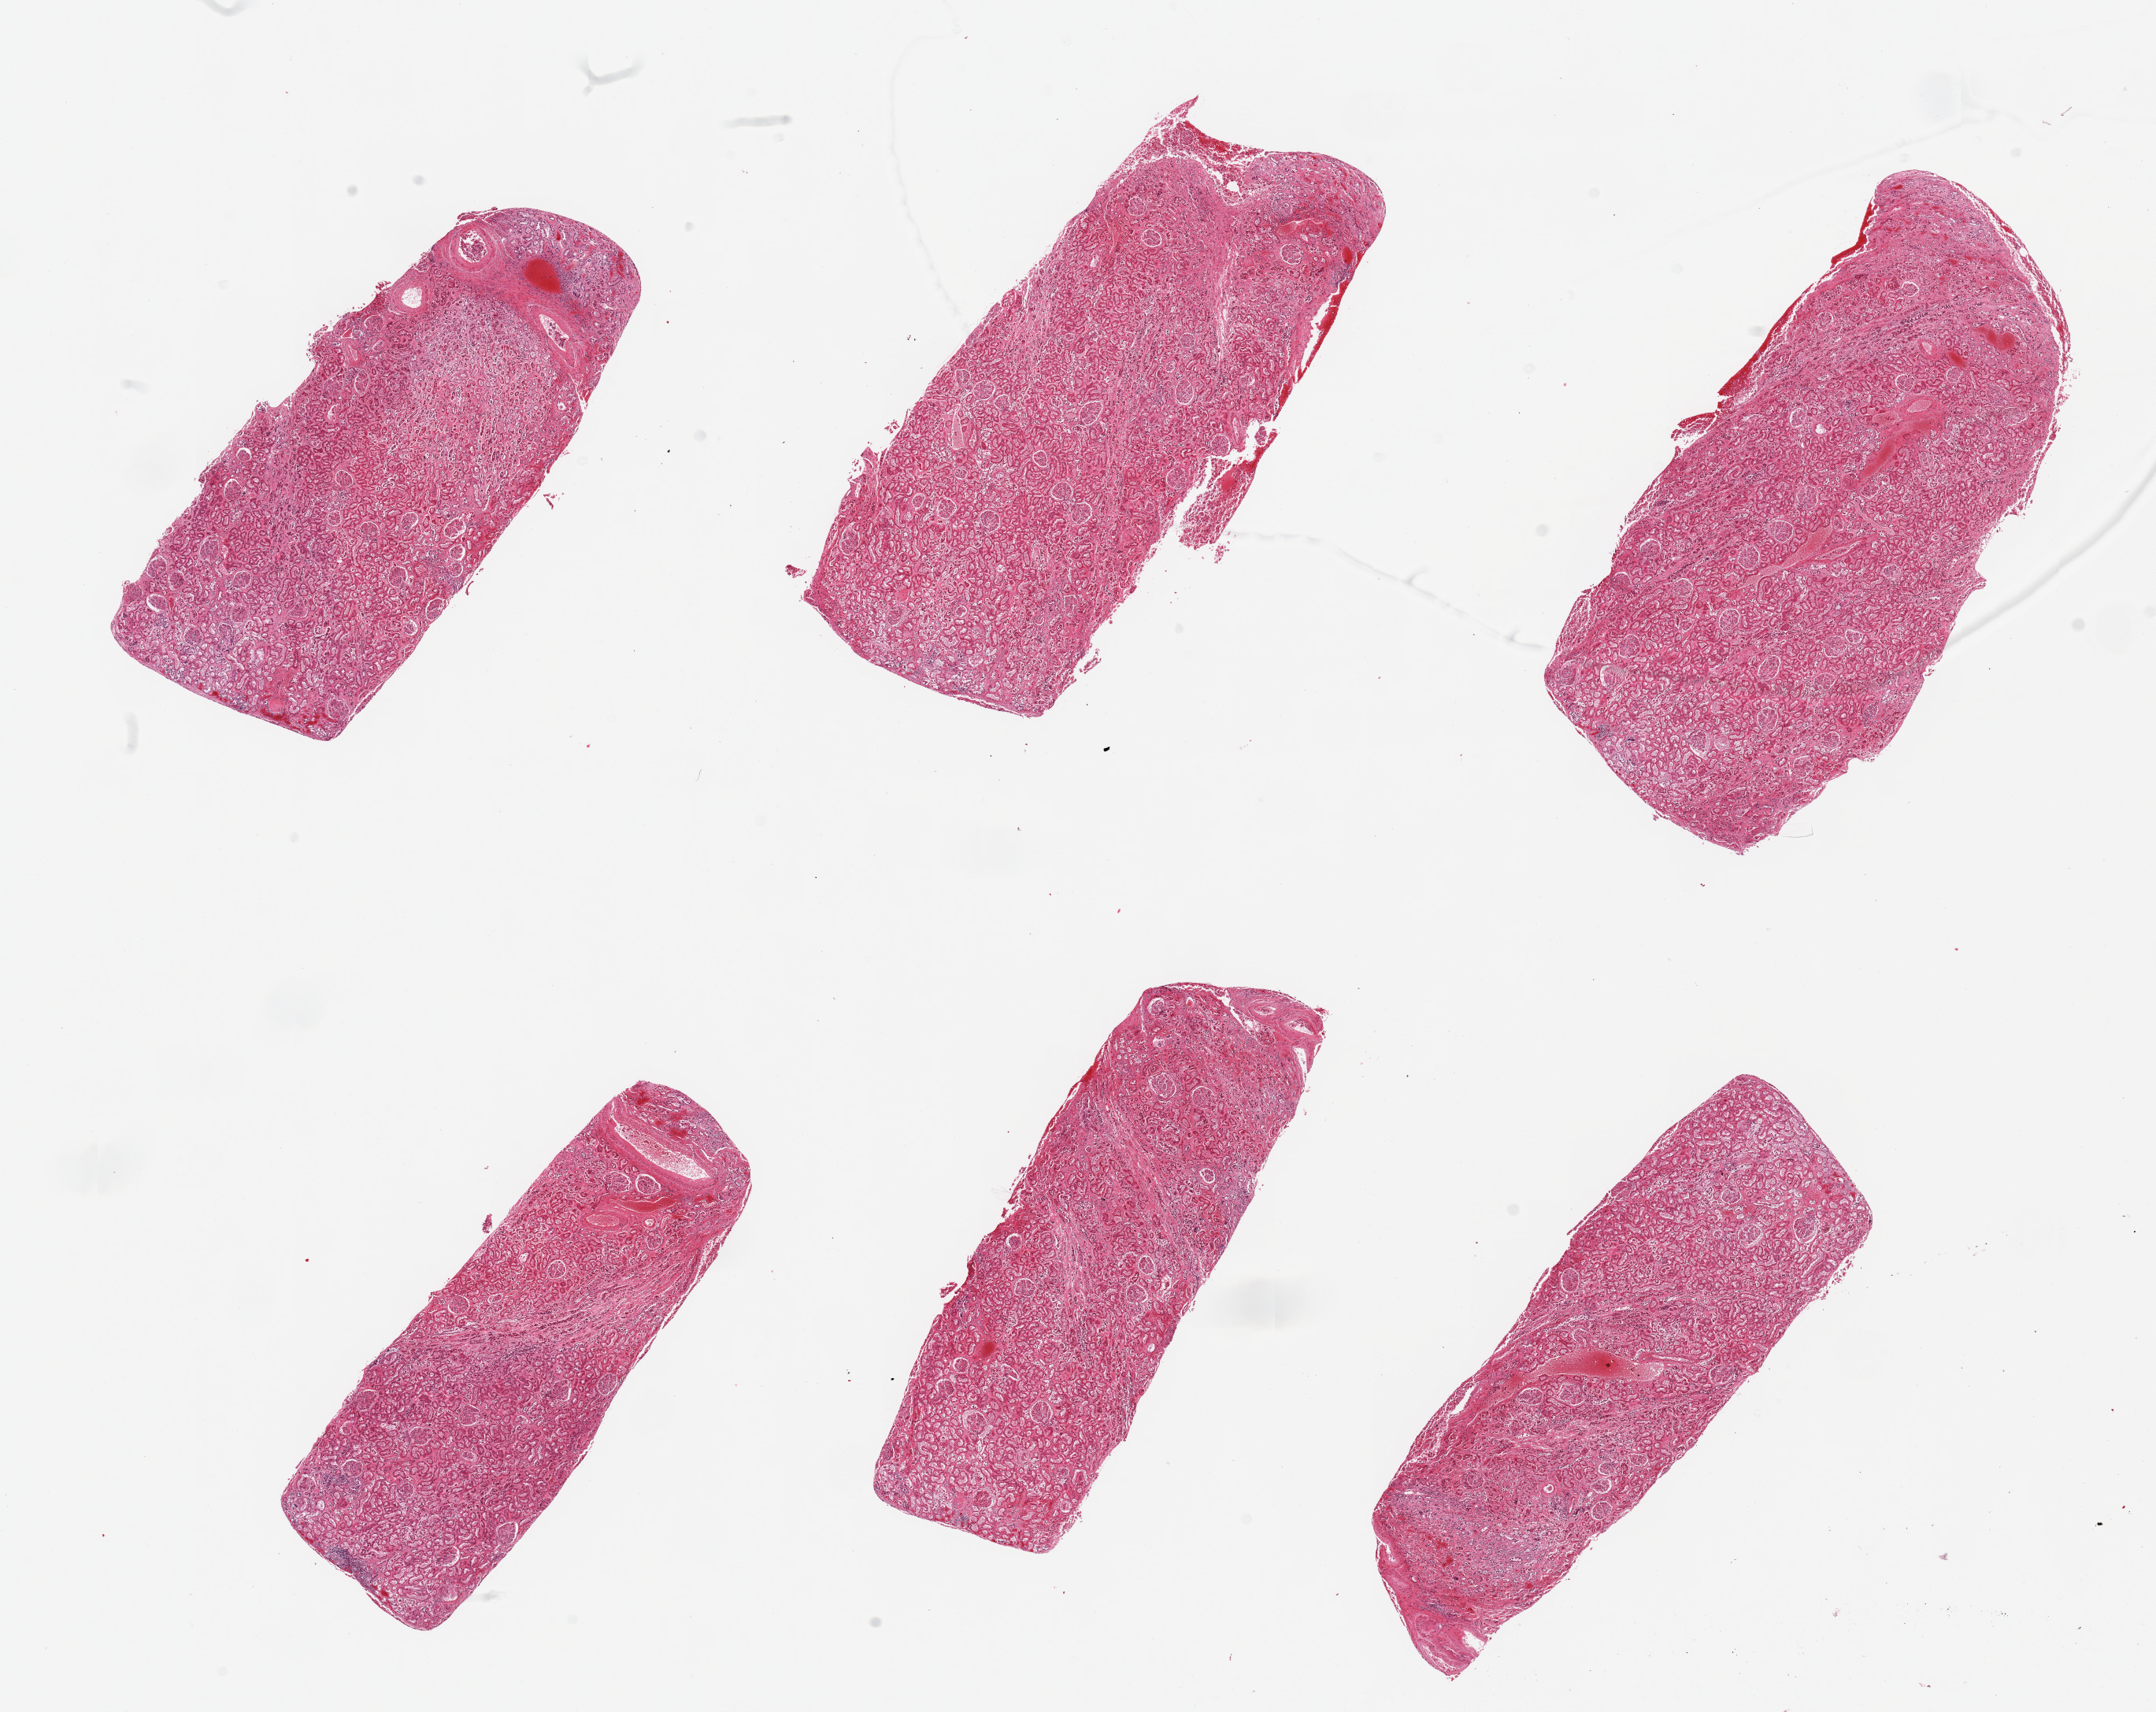
Digitized haematoxylin and eosin-stained section, shown as a low-resolution overview of the whole scanned area (about 21.7 x 17.2 mm); PAXgene-fixed paraffin-embedded (PFPE) section; section of renal cortex (target tissue); tissue donor sample. Donor sex: male.
• review note (as recorded): 6 pieces, glomeruli present, tubules modreately autolyzed